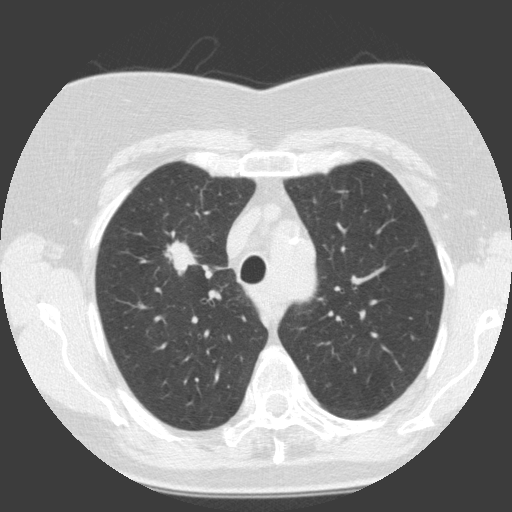
Low-dose screening chest CT, axial slice. Baseline annual screen. Lung window (W 1500 / L -600 HU). Standard (soft-tissue) reconstruction kernel (C). 120 kVp. 512 × 512 image matrix, field of view 300 × 300 mm. Female participant, aged 68 years at enrolment. Current smoker at enrolment.
Expert-annotated lung lesion, bounding box (x1, y1, x2, y2) in pixels: (156, 234, 208, 282). Screening reader's record for this exam (one nodule recorded; not confirmed to be the boxed lesion): non-calcified nodule or mass ≥4 mm, right upper lobe, 19 × 12 mm, smooth margins, soft tissue attenuation. Official screen result: positive, change unspecified: nodule(s) >= 4 mm or enlarging nodule(s), mass(es), or other non-specific abnormalities suspicious for lung cancer. Later outcome: lung cancer diagnosed 30 days after this screen — squamous cell carcinoma, NOS, right upper lobe, moderately differentiated (G2), stage IA (AJCC 6th edition), 28 mm at pathology.